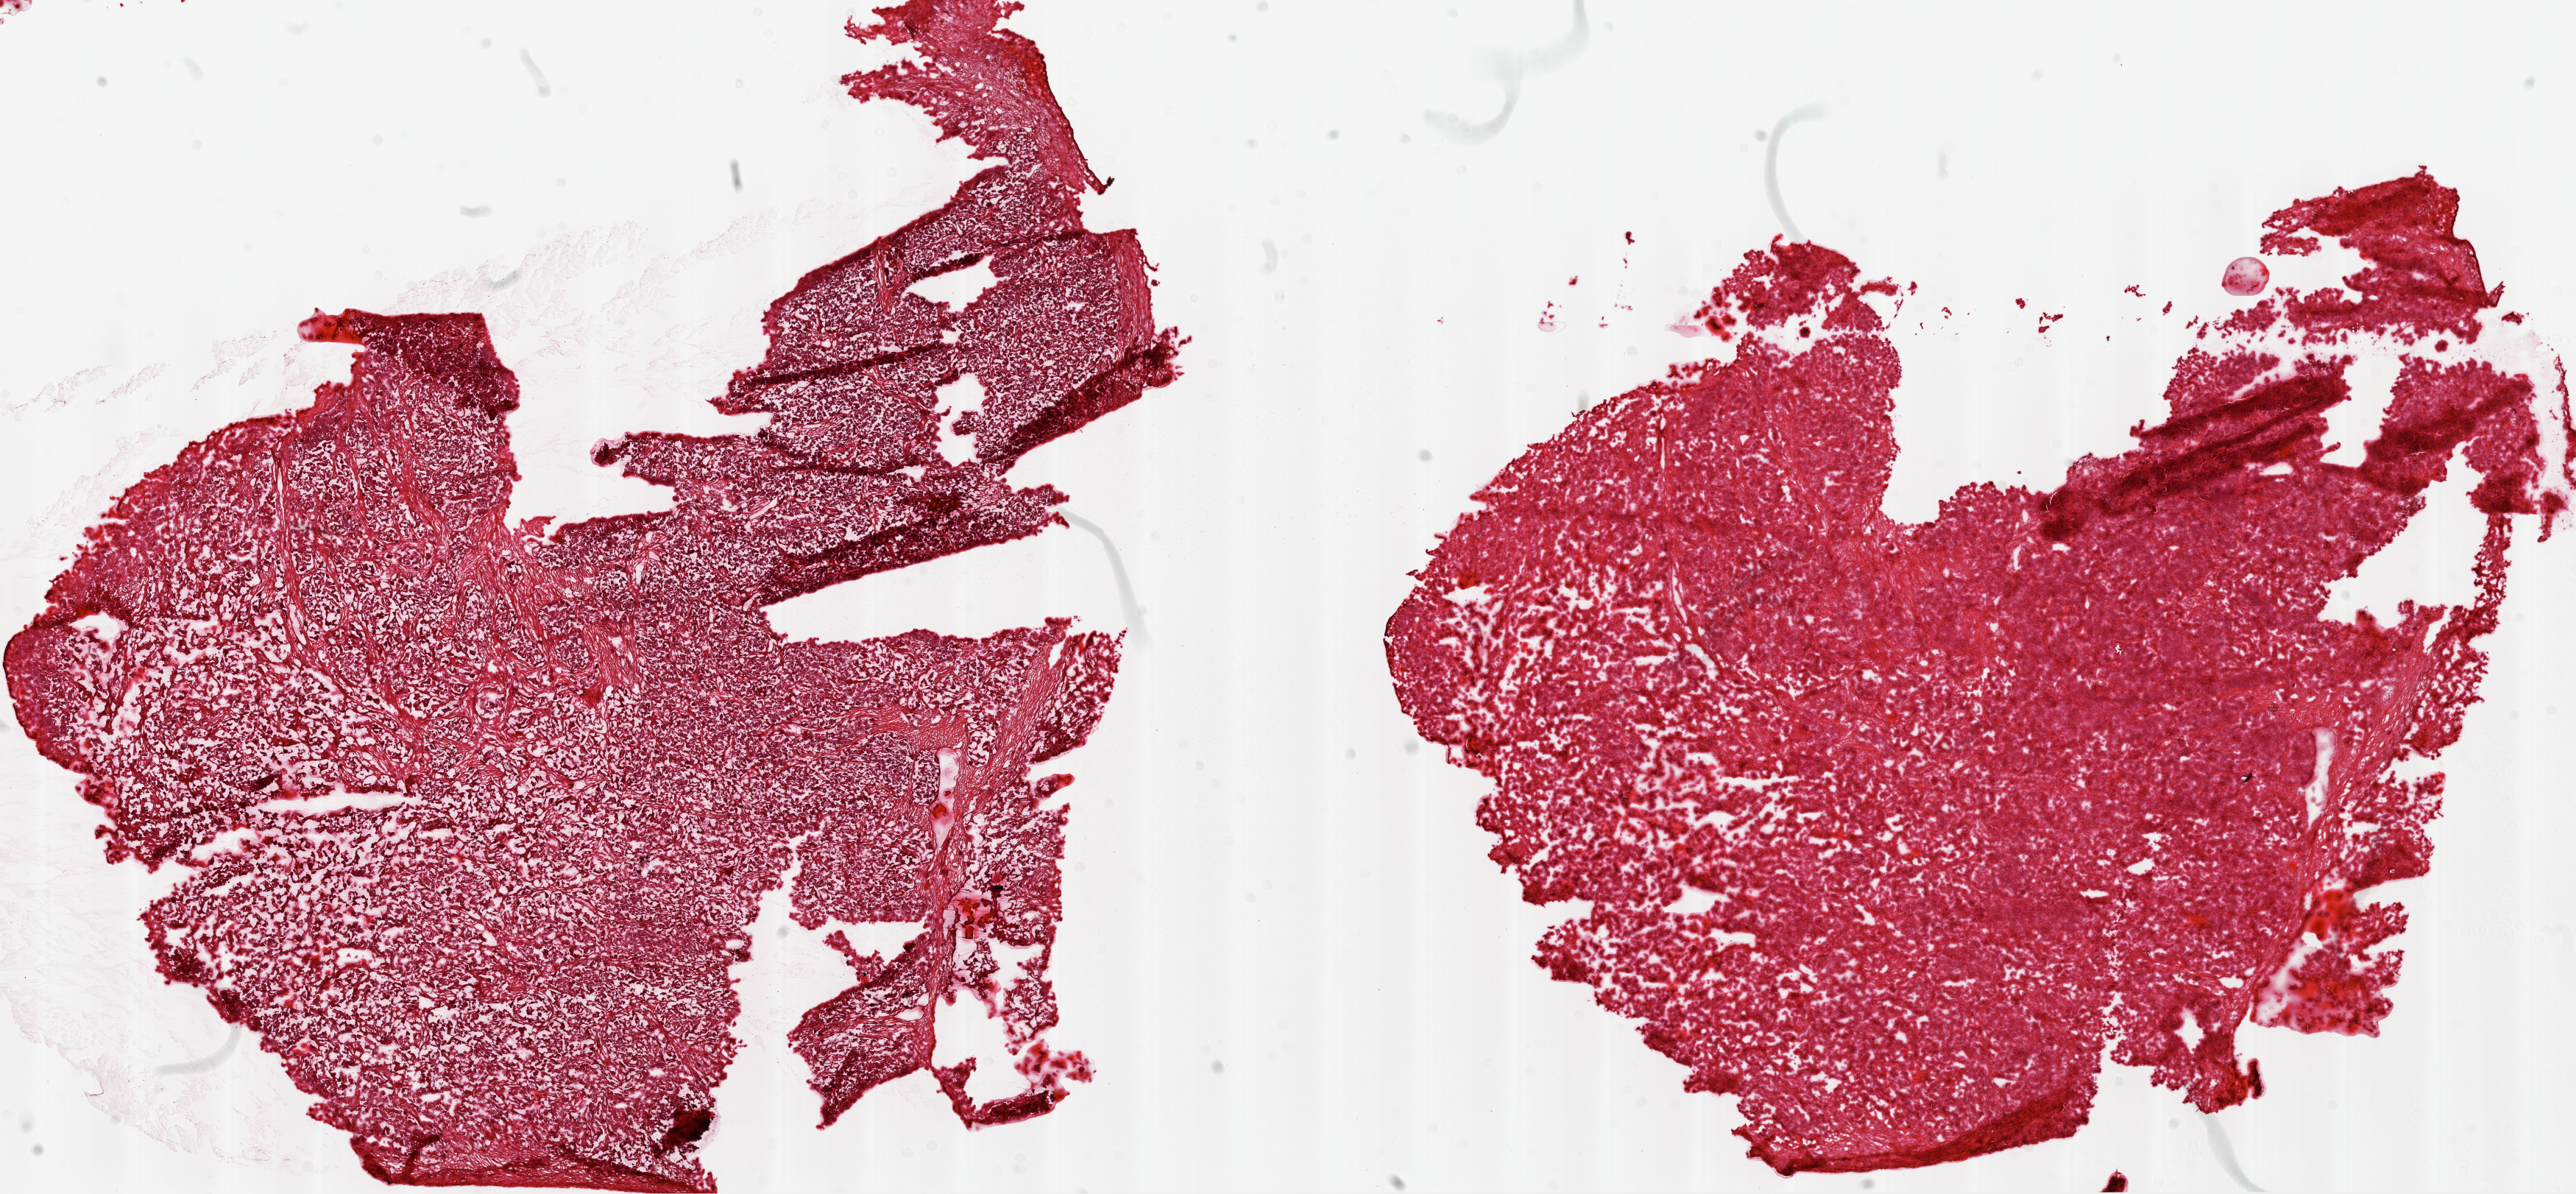
Hematoxylin and eosin (H&E) stained whole-slide image, shown as a low-resolution overview of the whole scanned area (about 28.1 x 13.0 mm, slide scanned at 20x); frozen section from the top of the tissue portion; sample: primary tumour, ovary. Female patient; age at initial diagnosis 57 years. Histologic grade: G3 (poorly differentiated). Pathologist review of this section (percent, as recorded): tumour cells 94%, tumour nuclei 95%, normal cells 0%, stromal cells 5%, necrosis 1%.
- FIGO stage: IIIC
- pathologic diagnosis: Serous cystadenocarcinoma, NOS